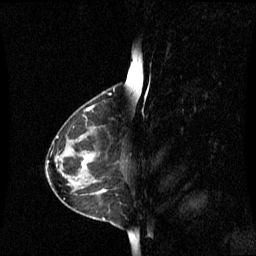
Breast MRI (dynamic contrast-enhanced), one sagittal slice. Position 36 of 60 along the scan axis. Dynamic contrast-enhanced series, image 2 of 3 at this slice position (ordered by acquisition). 1.5 T. TE 4.2 ms, TR 8.4 ms. 2.1 mm slice thickness. 256 × 256 image matrix. Female patient, age 42 years. Case-level facts recorded for this patient, not image findings: setting: breast cancer imaged before/during neoadjuvant chemotherapy; receptor status: HR-positive, HER2-negative.
Outlined on this slice (semi-automatically segmented with operator editing):
- analysis volume of interest (the breast-tissue region the enhancement analysis was run in; not a lesion): bounding box <60,126,106,195> (left, top, right, bottom; pixels)
- tumour enhancement mask (voxels above the 70 % enhancement threshold inside the analysis volume of interest): <81,156,93,167>